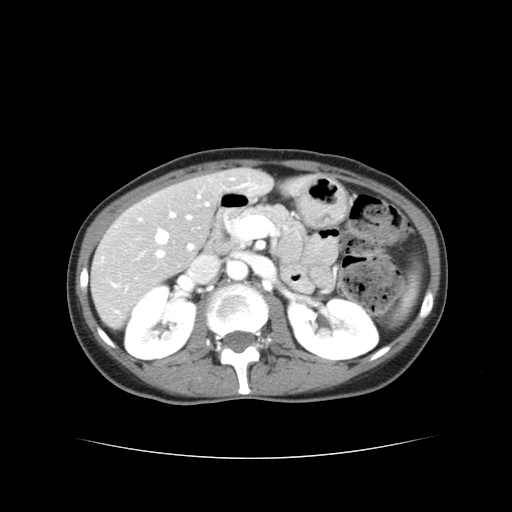
Contrast-enhanced abdominal CT, one axial slice. Position 18 of 38 along the scan axis. 120 kVp. Soft-tissue window (W 400 / L 40 HU). 512 × 512 image matrix, field of view 340 × 340 mm. Female patient, age 54 years. Case-level facts recorded for this patient, not image findings: diagnosis: colorectal cancer liver metastases, imaged before liver resection; multiple liver metastases: yes; largest metastasis: 1.1 cm; disease in both lobes: yes.
Outlined on this slice (manually delineated by an expert):
- hepatic veins: bounding box [x1, y1, x2, y2] px = [157, 196, 209, 244]
- liver: [91, 170, 299, 324]
- planned liver remnant (the part of the liver to remain after resection): [220, 171, 272, 193]
- portal vein (with intrahepatic branches): [157, 214, 193, 257]